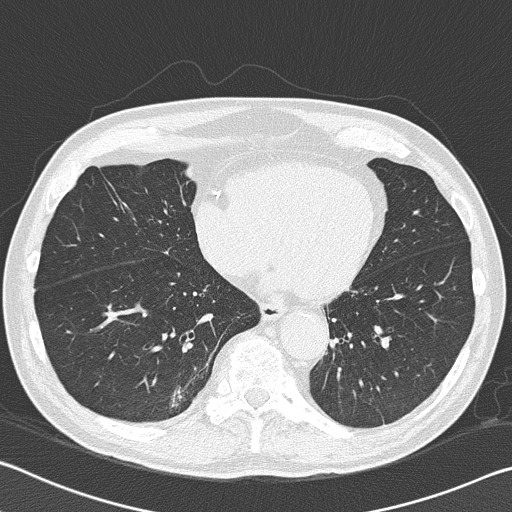
Low-dose screening chest CT, axial slice; baseline annual screen; lung window (W 1500 / L -600 HU); 2 mm slice thickness; 120 kVp; 512 × 512 image matrix. Male participant, aged 74 years at enrolment. Current smoker at enrolment.
• Expert-annotated lung lesion, bounding box <147,369,213,430> (left, top, right, bottom; pixels).
• The exam's reader record, not a measurement of the box and not confirmed to be the same lesion: non-calcified nodule or mass ≥4 mm, right lower lobe, 13 × 11 mm, spiculated (stellate) margins, soft tissue attenuation.
• Official screen result: positive, change unspecified: nodule(s) >= 4 mm or enlarging nodule(s), mass(es), or other non-specific abnormalities suspicious for lung cancer.
• Lung cancer was diagnosed 414 days after this screen (after the second annual screen): bronchiolo-alveolar adenocarcinoma, NOS, right lower lobe, moderately differentiated (G2), stage IA (AJCC 6th edition), 16 mm at pathology.